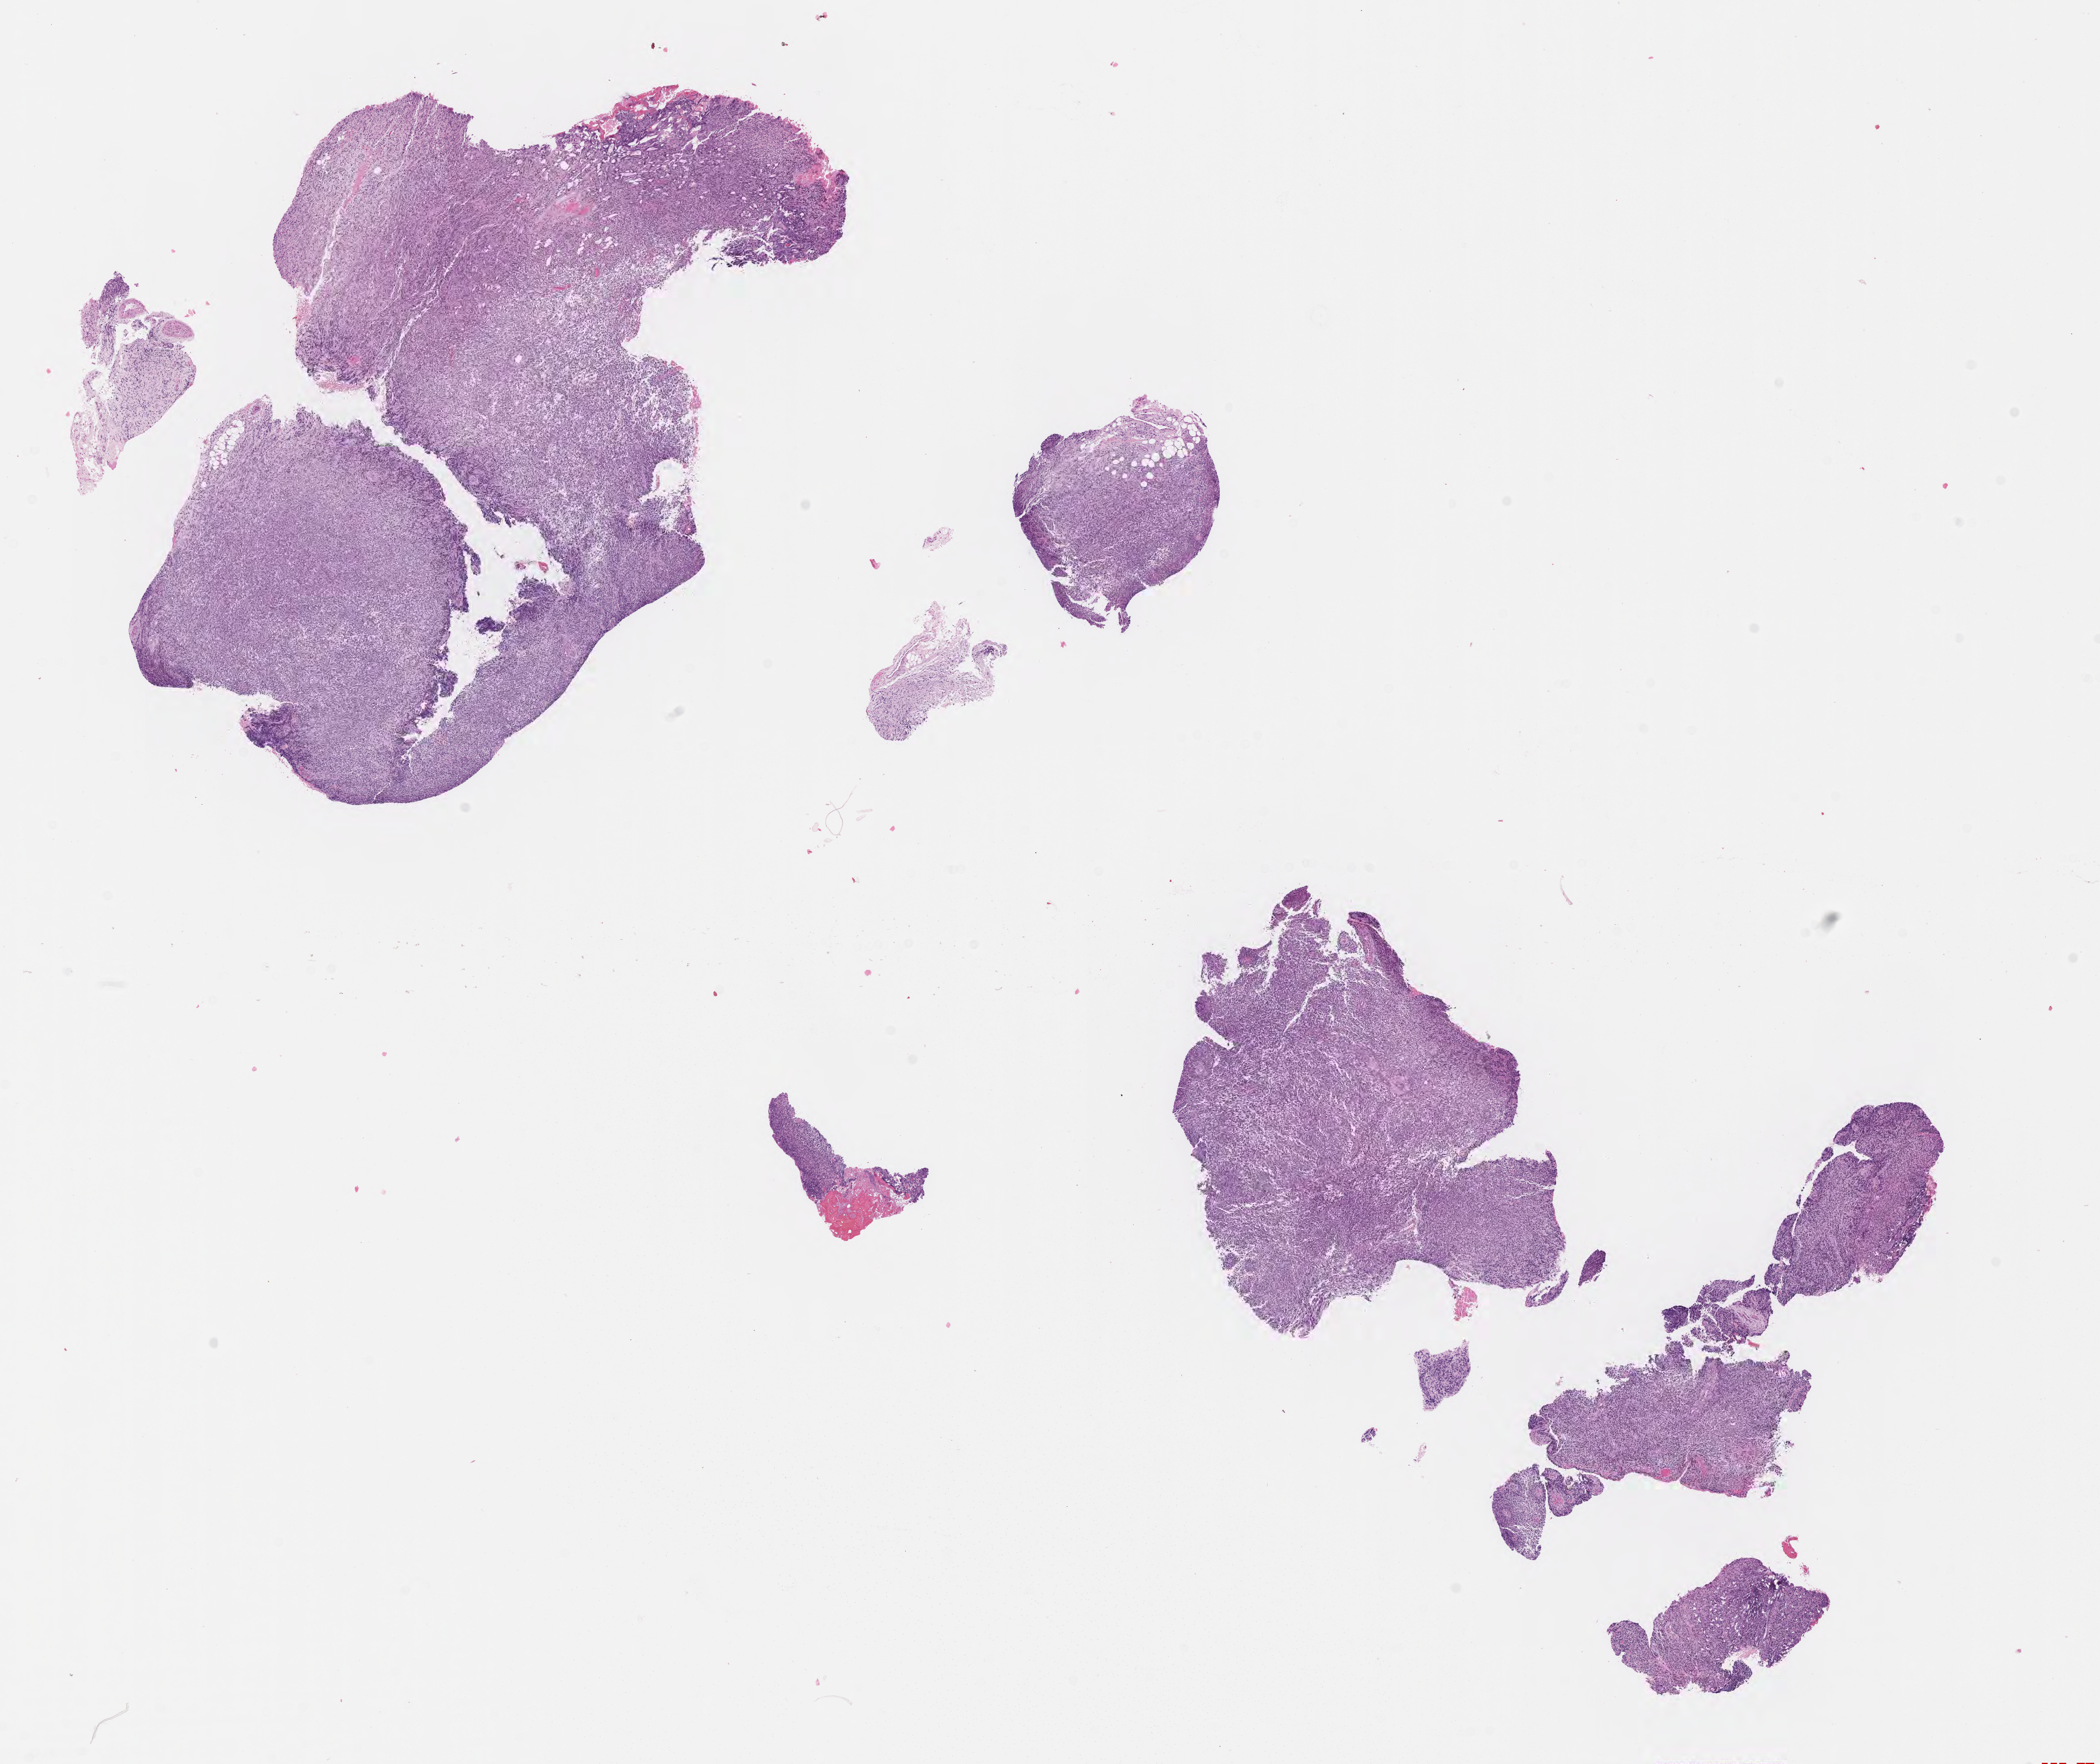
Whole-slide image, hematoxylin and eosin (H&E) stain of tumor tissue, a low-resolution overview of the entire scanned area, about 14.6 x 12.3 mm; formalin-fixed, paraffin-embedded (FFPE) tissue; site: orbit, right. Female patient, age at diagnosis 6.3 years.
Stage (as recorded): 1. Metastatic status at presentation (as recorded): non-metastatic. Diagnosis: rhabdomyosarcoma; histological classification: spindle cell rhabdomyosarcoma.